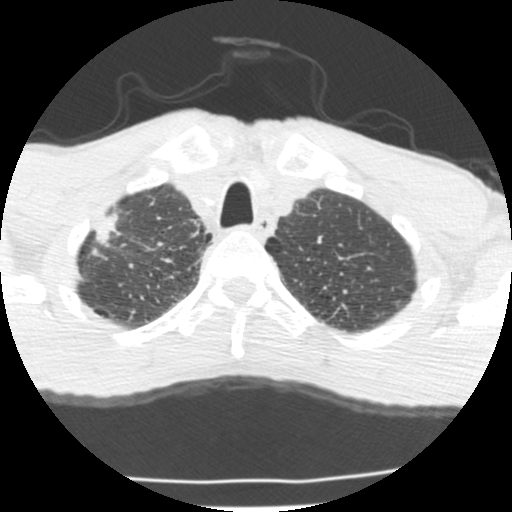
Low-dose screening chest CT, one axial slice; position 184 of 214 along the scan axis; reconstruction kernel STANDARD; lung window (W 1500 / L -600 HU); 2.5 mm slice thickness; 512 × 512 image matrix.
Annotated regions visible in this slice (expert manual segmentation):
- lesion 1 (tumor, upper lobe of right lung): bounding box (x1, y1, x2, y2) in pixels: (95, 214, 119, 247)